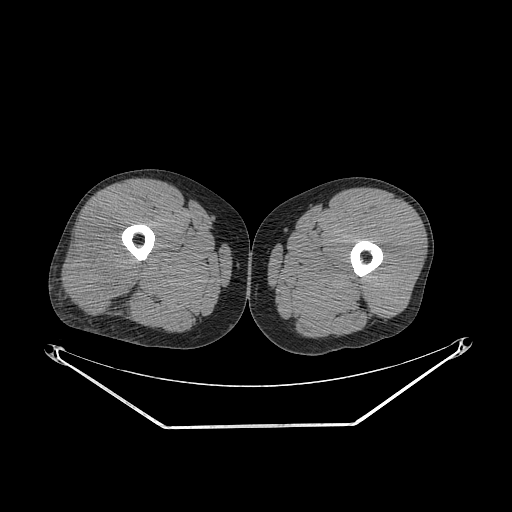
CT of an extremity soft-tissue mass (from a PET/CT study), one axial slice. Position 247 of 267 along the scan axis. Reconstruction kernel STANDARD. Soft-tissue window (W 400 / L 40 HU). 512 × 512 image matrix. Male patient. From the clinical record (not read from this slice): histological type: poorly differentiated synovial sarcoma; grade: high; site of the primary tumour: right buttock.
Annotated regions visible in this slice (expert contour drawn on MRI and transferred to this co-registered scan by the dataset authors):
- gross tumour volume including surrounding oedema: box from (x=62, y=221) to (x=140, y=312) px
- gross tumour volume (mass): (x=62, y=221)–(x=138, y=309)